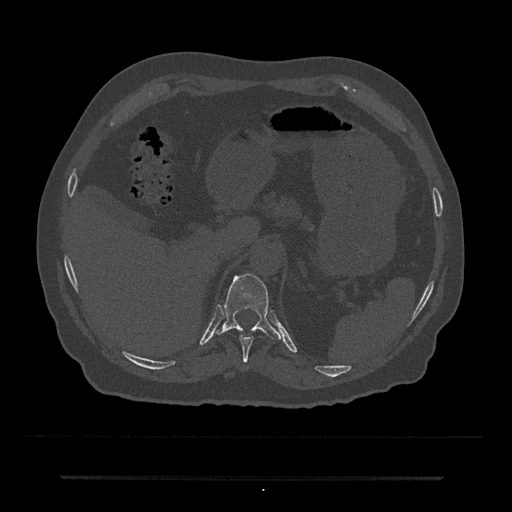
CT including the spine, one axial slice; position 195 of 797 along the scan axis; 120 kVp; bone window (W 1800 / L 400 HU); 0.5 mm slice thickness; 512 × 512 image matrix, field of view 437 × 437 mm. Patient: male, 69 years. From the clinical record (not read from this slice): primary cancer: prostate.
Outlined on this slice (semi-automatically segmented with operator editing):
- T10 vertebra: bounding box <239,335,254,362> (left, top, right, bottom; pixels)
- T11 vertebra: <215,273,282,340>